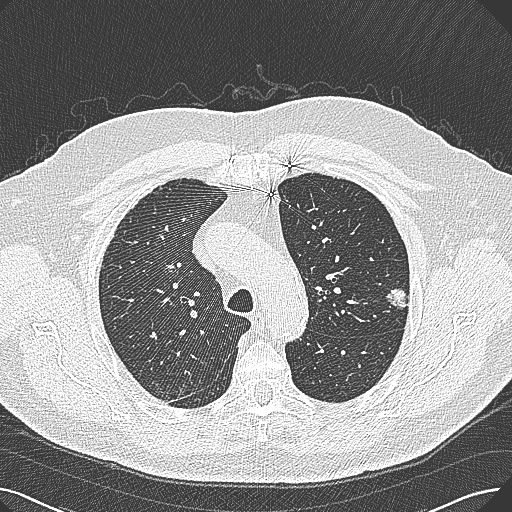
Axial slice from a low-dose chest CT screening exam; first (baseline) screen; lung window (W 1500 / L -600 HU); 1 mm slice thickness; 120 kVp; slice 76 of 269 in the series. Male, age 74 years at enrolment. Former smoker at enrolment.
Expert reader's lesion annotation, box from (x=375, y=273) to (x=423, y=318) px. Screening reader's record for this exam (one nodule recorded; not confirmed to be the boxed lesion): non-calcified nodule or mass ≥4 mm, left upper lobe, 15 × 10 mm, poorly defined margins, soft tissue attenuation. Official screen result: positive, change unspecified: nodule(s) >= 4 mm or enlarging nodule(s), mass(es), or other non-specific abnormalities suspicious for lung cancer.